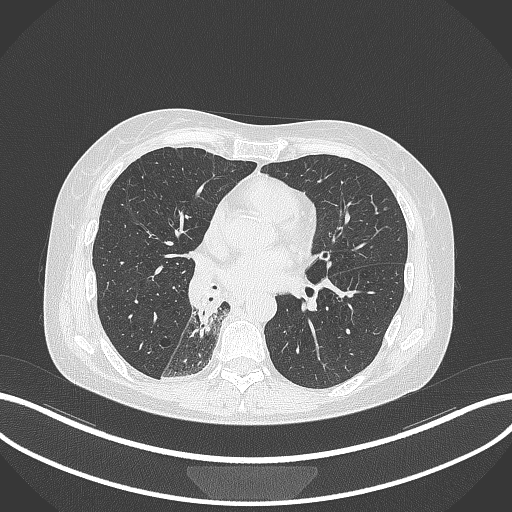
Chest CT, one axial slice. Slice 144 of 329 in the series (ordered by position). Lung window (W 1500 / L -600 HU). 1 mm slice thickness. 512 × 512 image matrix, field of view 400 × 400 mm. Female patient, age 63 years. From the clinical record (not read from this slice): clinical TNM (as recorded): T1c N0 M0.
Outlined on this slice (rectangle marked by the reading radiologist):
- lung tumour (recorded histology: adenocarcinoma): box from (x=194, y=278) to (x=220, y=336) px